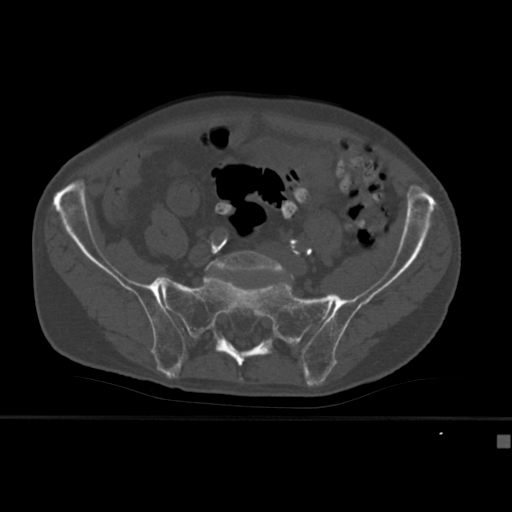
CT including the spine, one axial slice. Slice 70 of 430 in the series (ordered by position). Bone window (W 1800 / L 400 HU). 1.5 mm slice thickness. 512 × 512 image matrix. Male patient, age 64 years. Case-level facts recorded for this patient, not image findings: primary cancer: uterus.
Outlined on this slice (semi-automatic segmentation, software-assisted and operator-edited):
- L5 vertebra: bounding box [x1, y1, x2, y2] px = [204, 251, 295, 281]